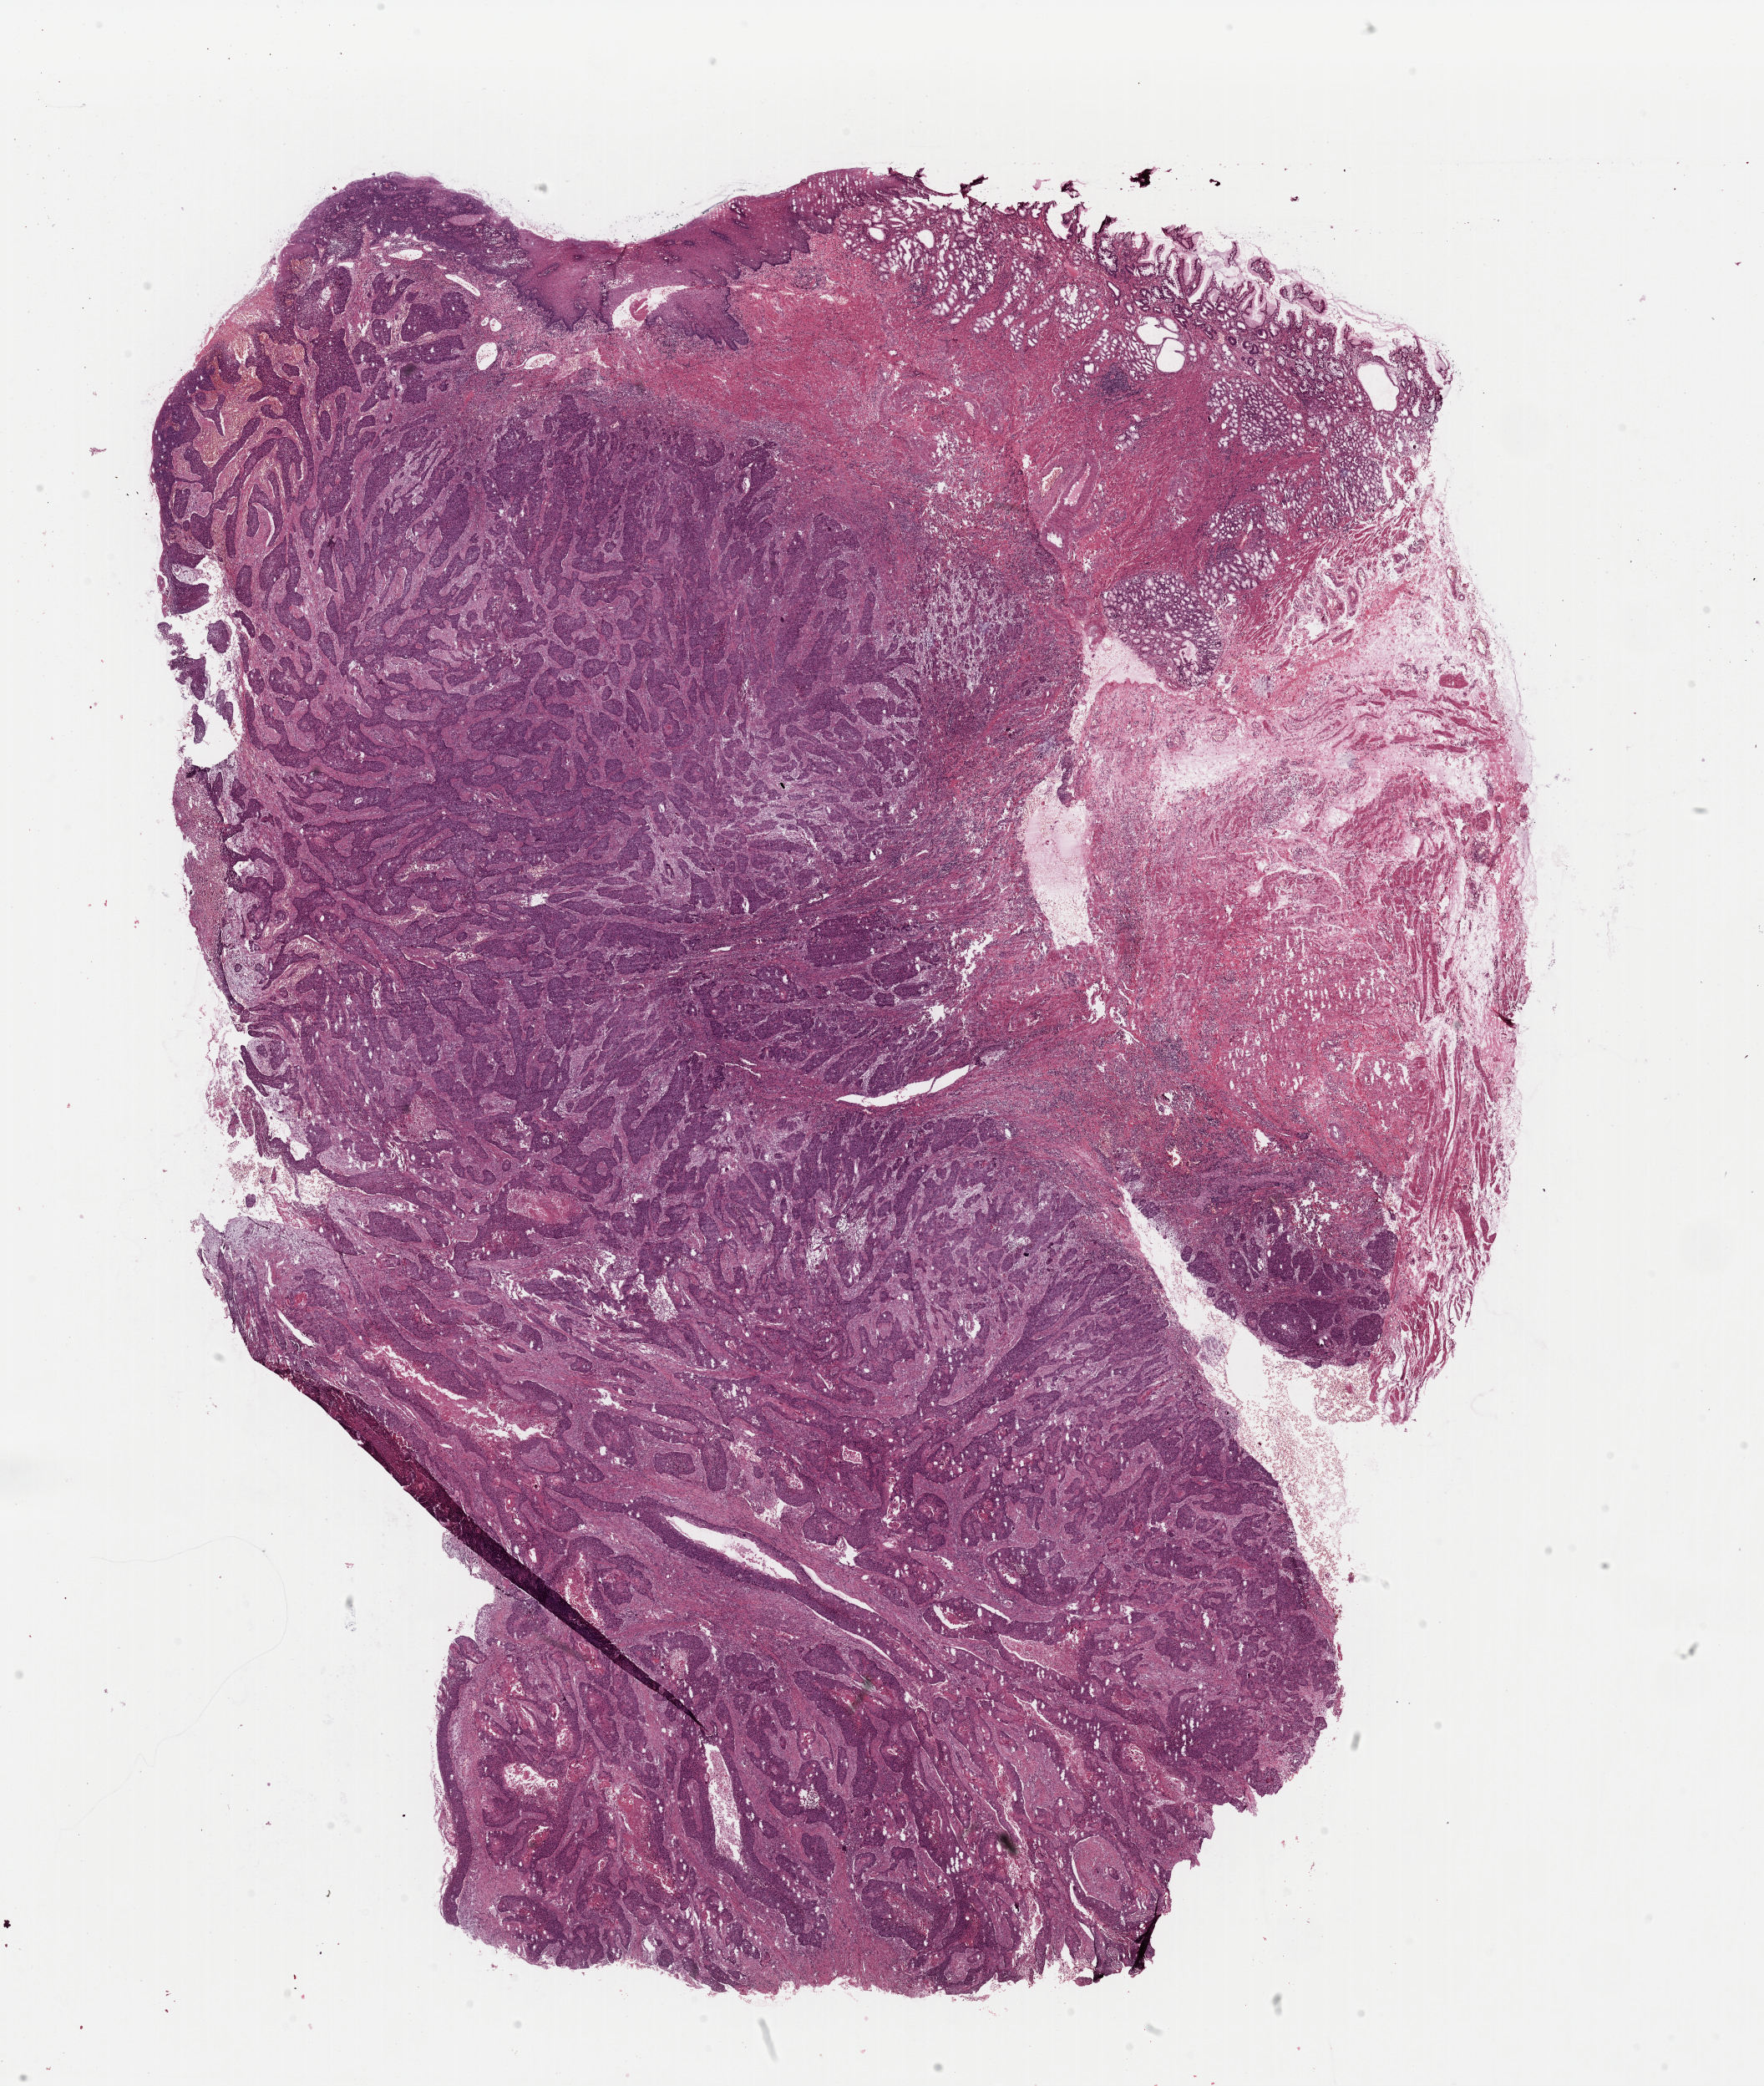
Hematoxylin and eosin (H&E) stained whole-slide image — low-resolution overview of the scanned area, about 16.7 x 19.7 mm. FFPE section. Primary tumour sample from the esophagus. Male patient; age at initial diagnosis 65 years. Histologic grade: G2 (moderately differentiated).
- AJCC pathologic stage: II
- TNM: T2 N0 M0
- pathologic diagnosis: Squamous cell carcinoma, NOS (lower third of esophagus)